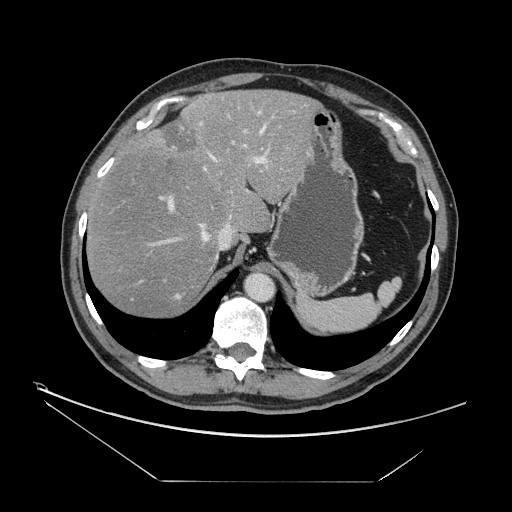
Contrast-enhanced abdominal CT, one axial slice. Slice 115 of 161 in the series (ordered by position). 120 kVp. Intravenous contrast given. Soft-tissue window (W 400 / L 40 HU). 512 × 512 image matrix, field of view 440 × 440 mm. Male patient, age 65 years. Case-level facts recorded for this patient, not image findings: diagnosis: colorectal cancer liver metastases, imaged before liver resection; multiple liver metastases: yes; largest metastasis: 4.2 cm; chemotherapy before resection: yes.
Structures marked on this image (outlined manually by an expert reader):
- hepatic veins: box from (x=152, y=126) to (x=265, y=259) px
- liver: (x=87, y=91)–(x=316, y=318)
- planned liver remnant (the part of the liver to remain after resection): (x=87, y=91)–(x=315, y=318)
- portal vein (with intrahepatic branches): (x=159, y=105)–(x=306, y=226)
- liver metastasis: (x=161, y=121)–(x=198, y=155)